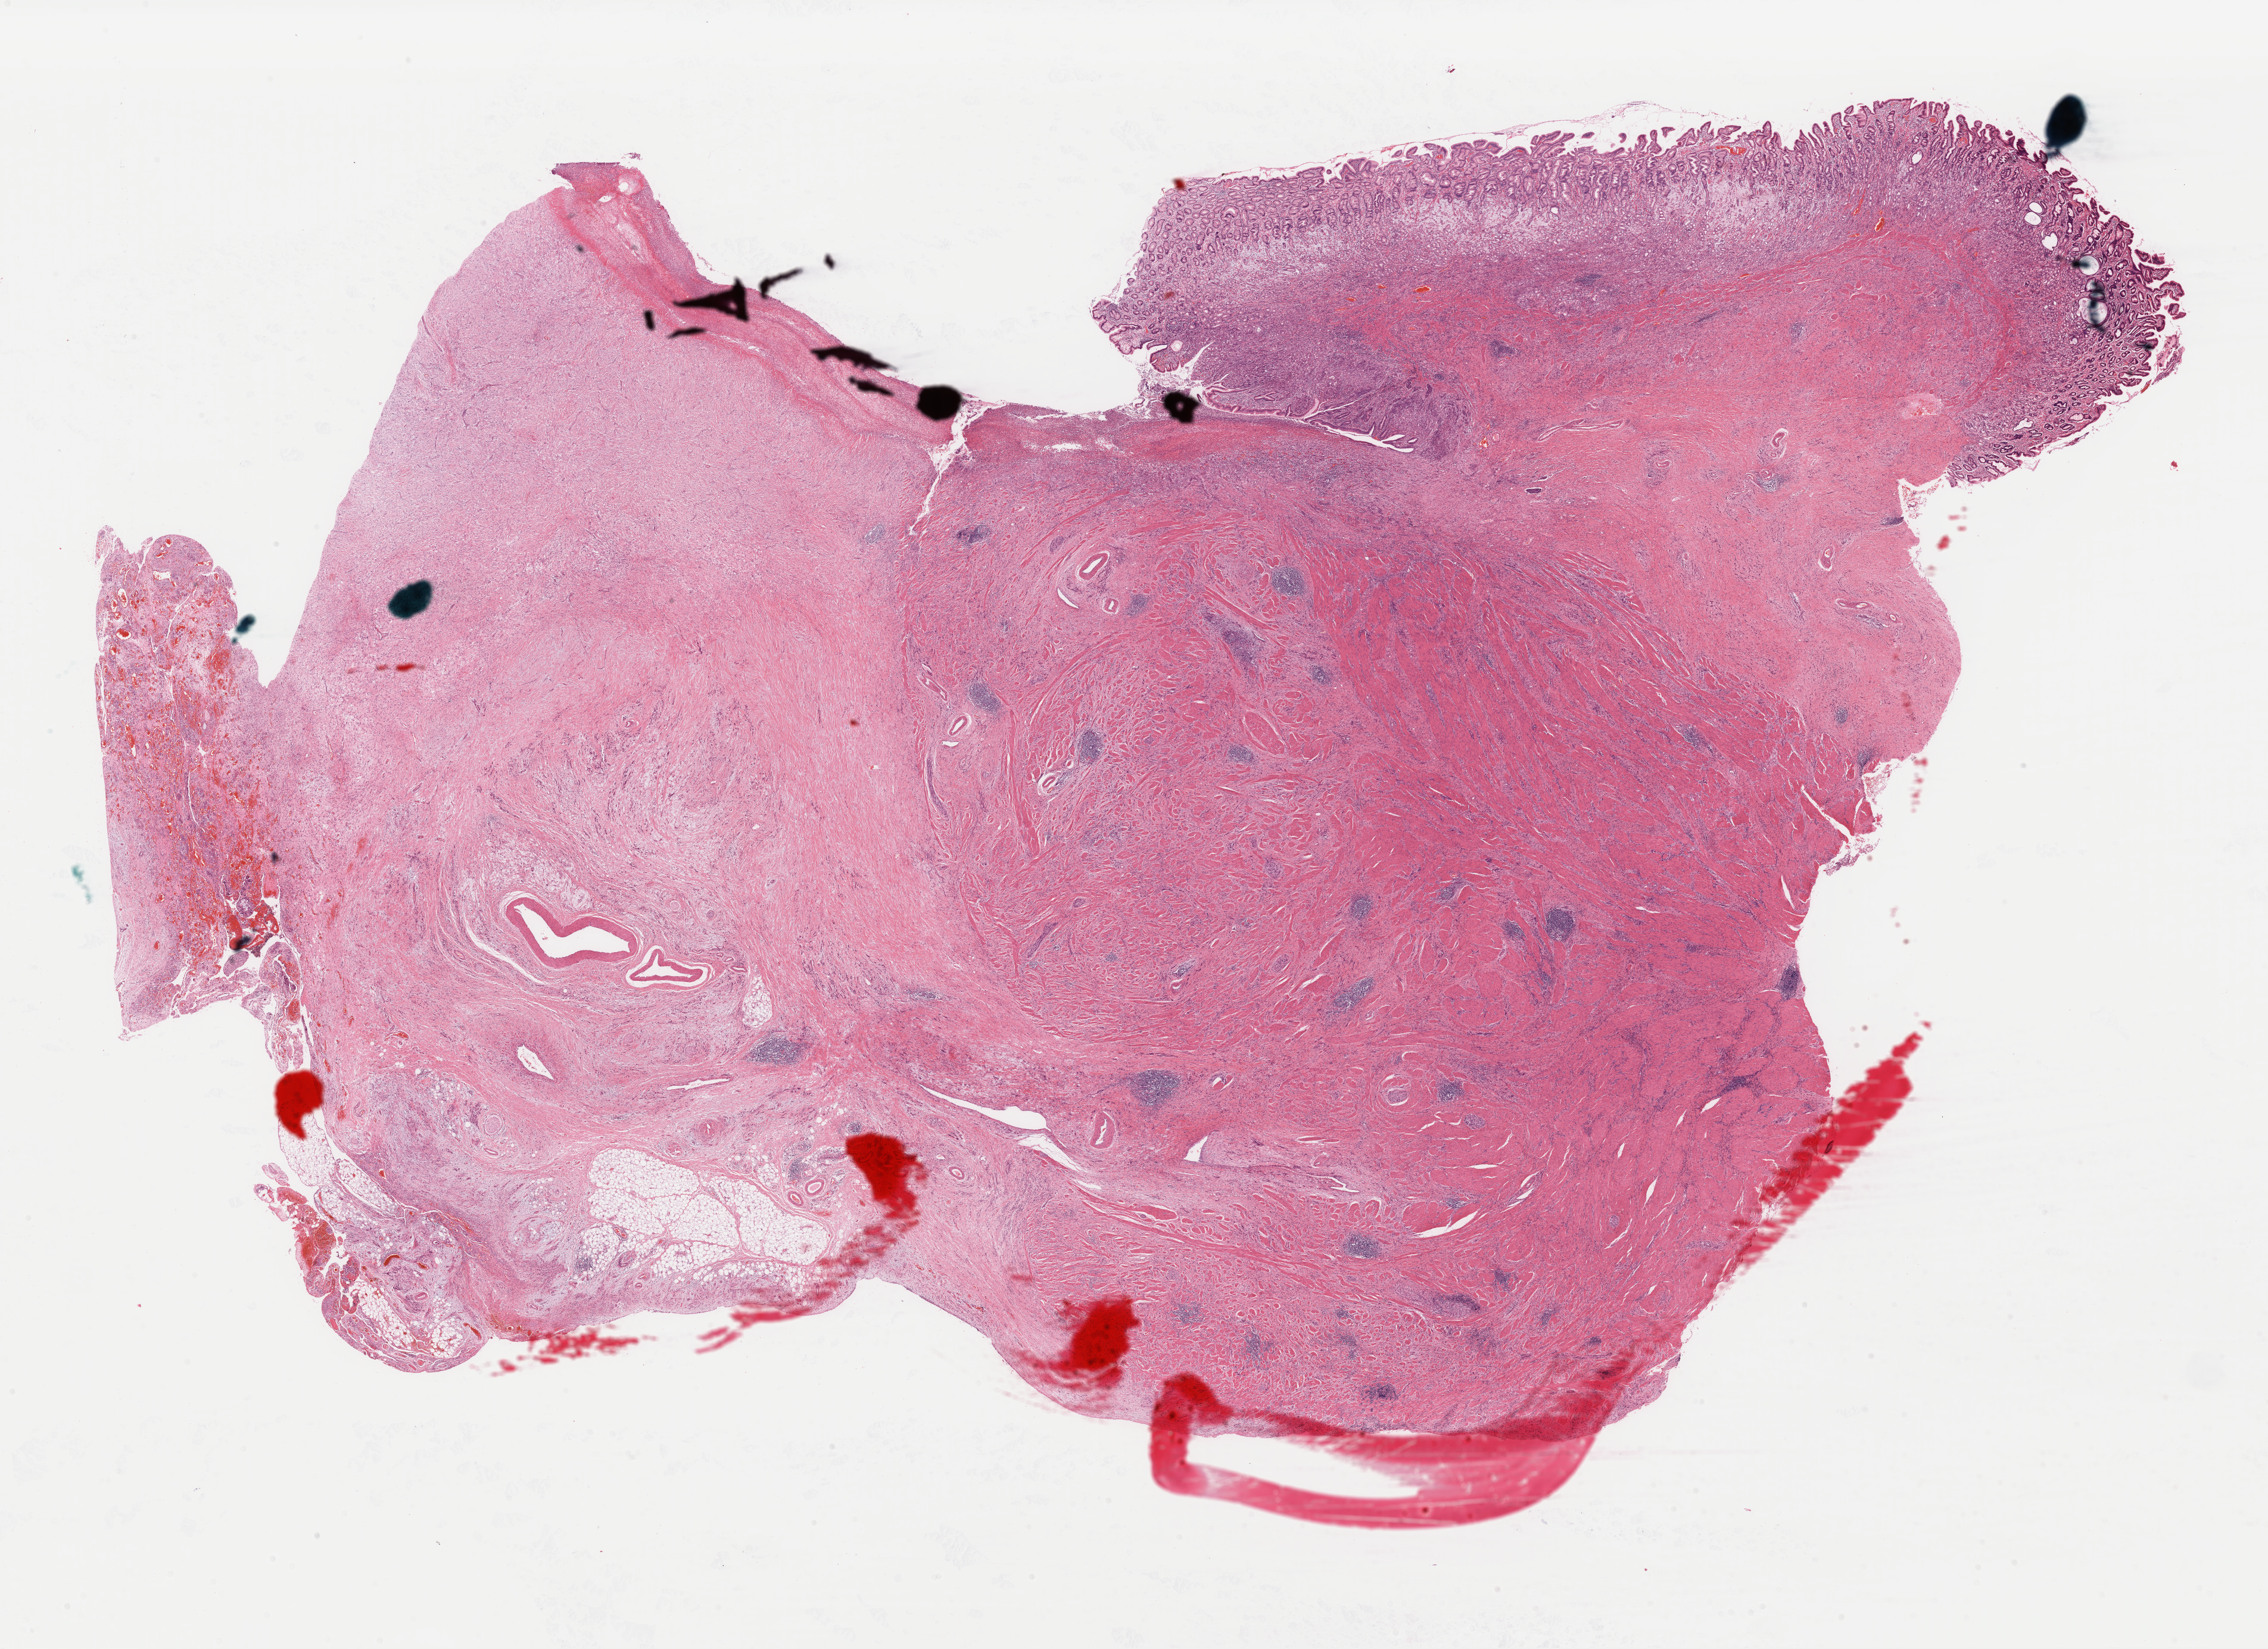
Digitized H&E tissue section (whole slide) — shown as a low-resolution overview of the whole scanned area (about 30.1 x 21.9 mm, slide scanned at 40x); formalin-fixed paraffin-embedded (FFPE) diagnostic section; primary tumour sample from the stomach. Female, age 45 years at initial diagnosis. Histologic grade: G3 (poorly differentiated).
Pathologic diagnosis: Carcinoma, diffuse type (gastric antrum). Lymph nodes positive (case pathology): 3 of 5 examined. AJCC pathologic stage: IIIB (7th edition).